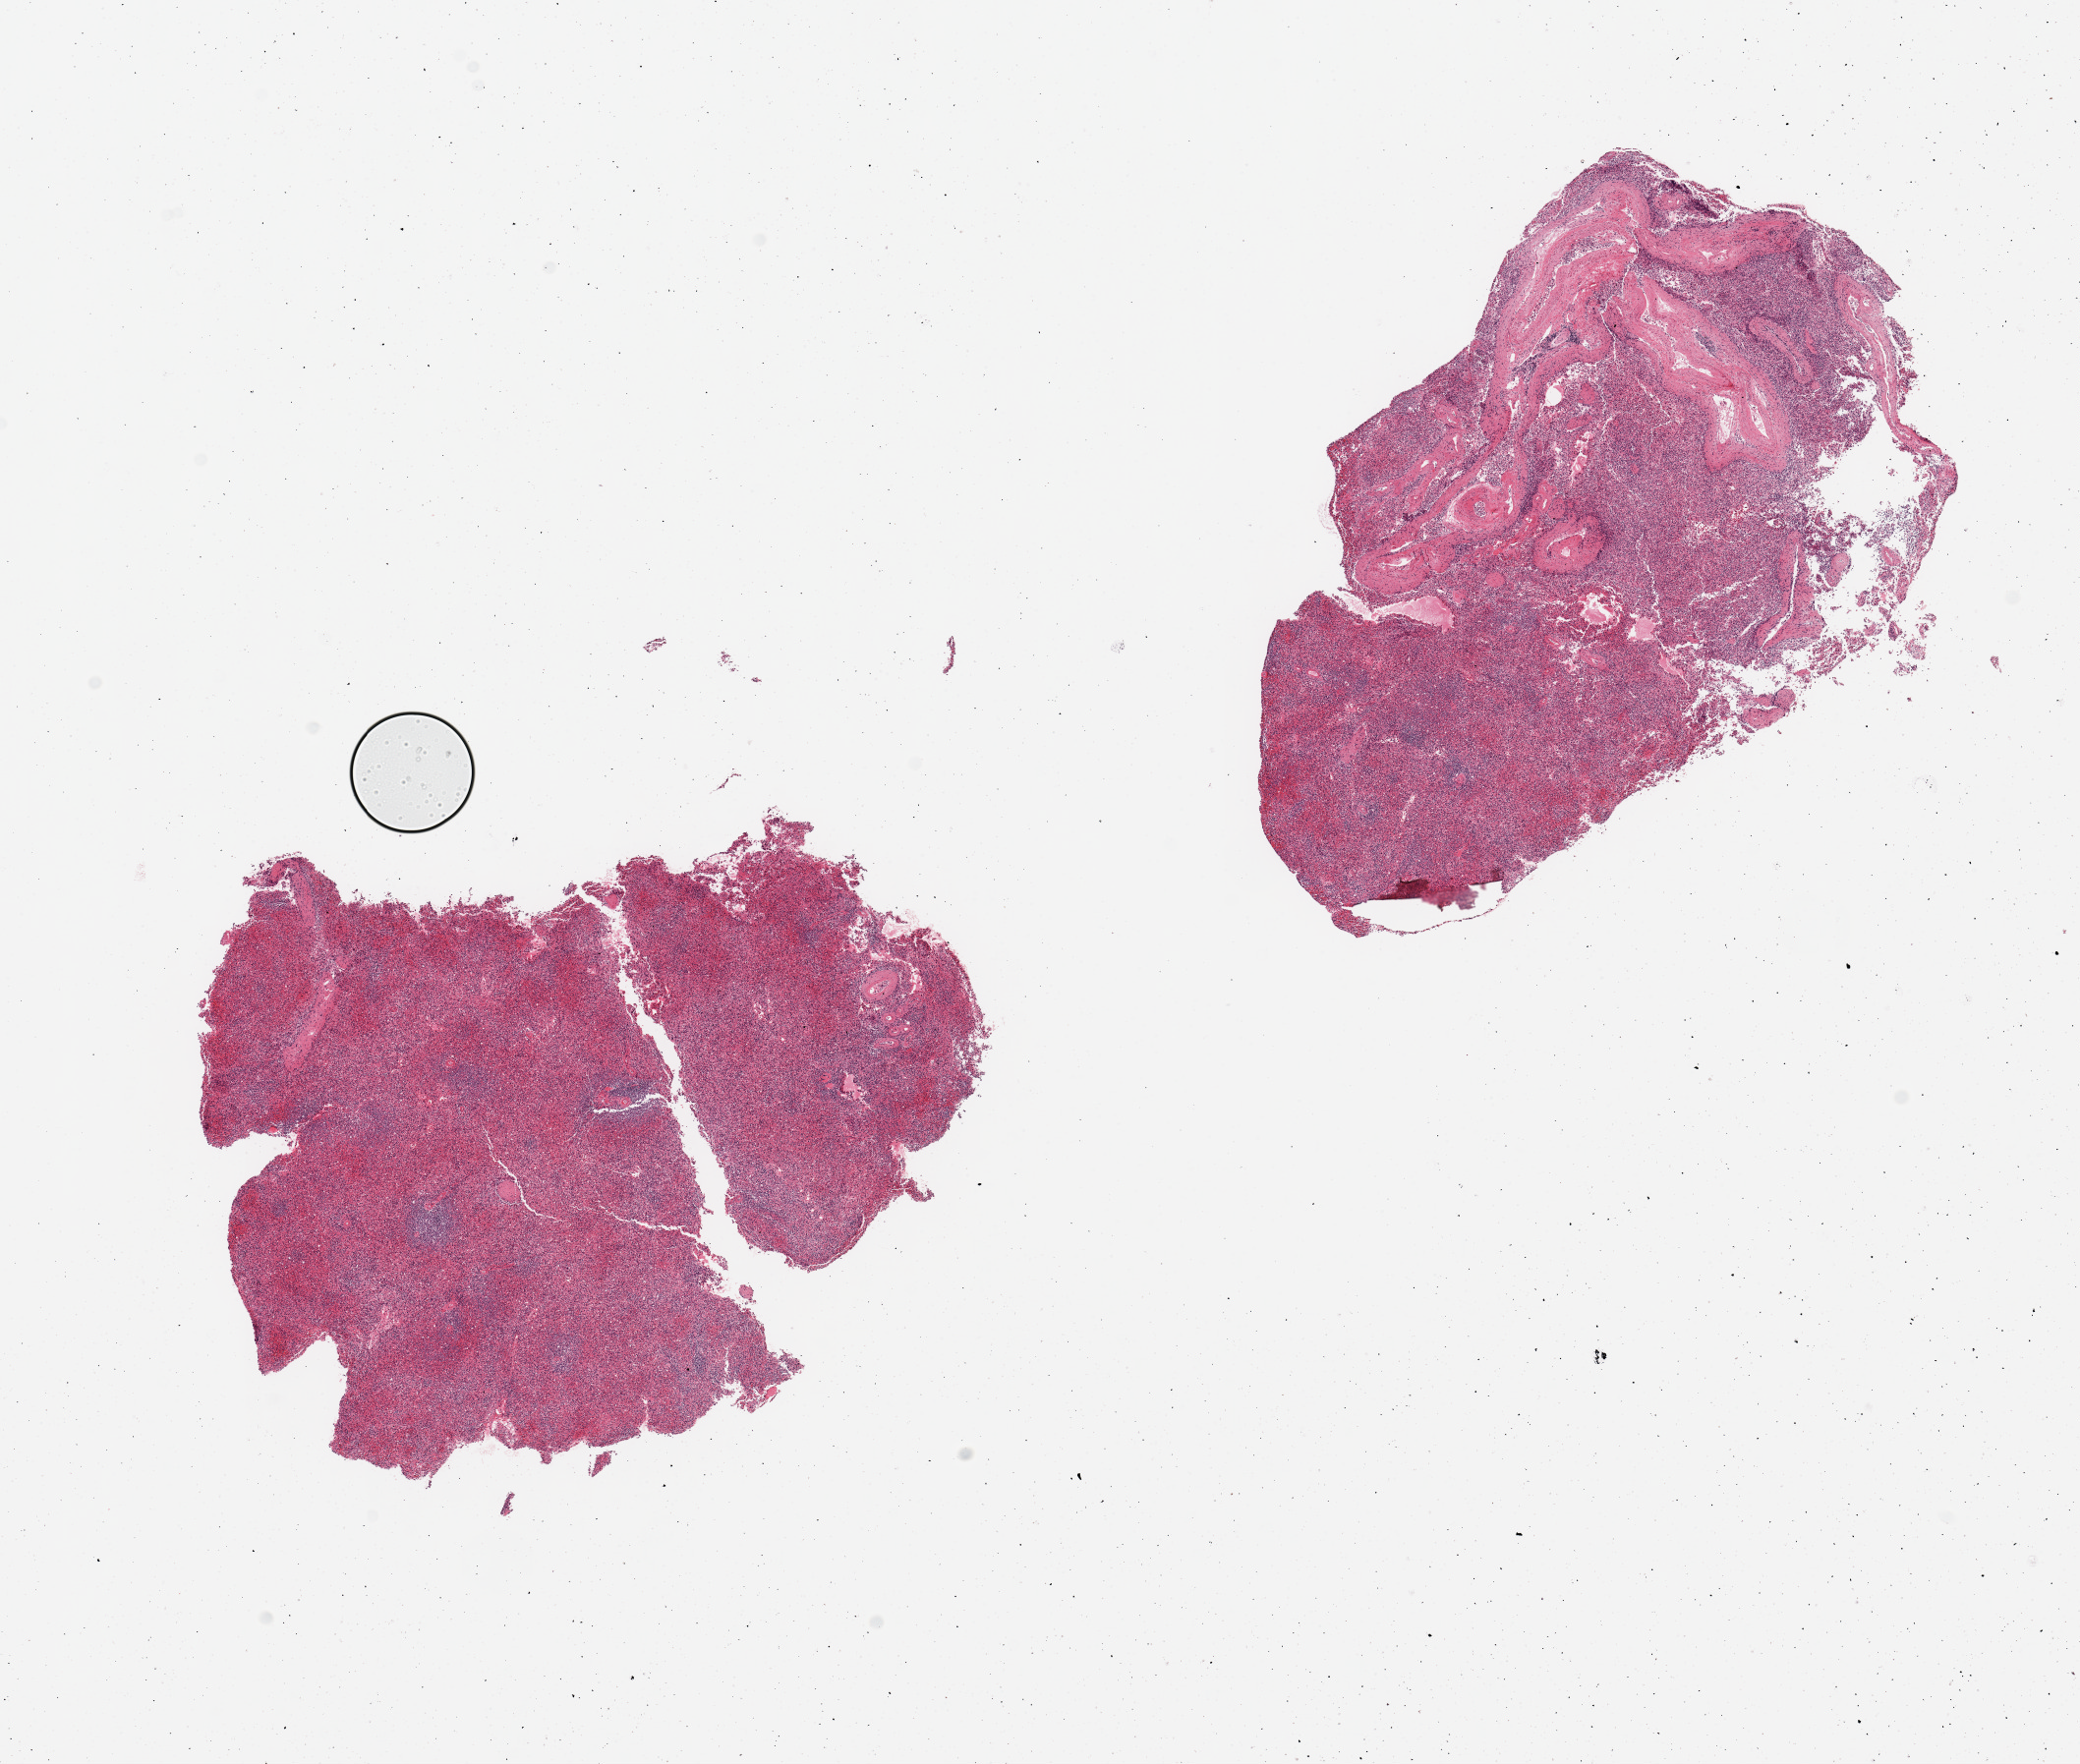
Whole-slide image, haematoxylin and eosin stain, whole scanned area (about 16.7 x 14.2 mm, acquisition: 20x scan) shown as a low-resolution overview, PAXgene-fixed, paraffin-embedded tissue, target tissue: spleen, tissue donor sample.
Reviewer comment on this tissue sample: 2 pieces; large vessels comprise 20% of 1 piece.